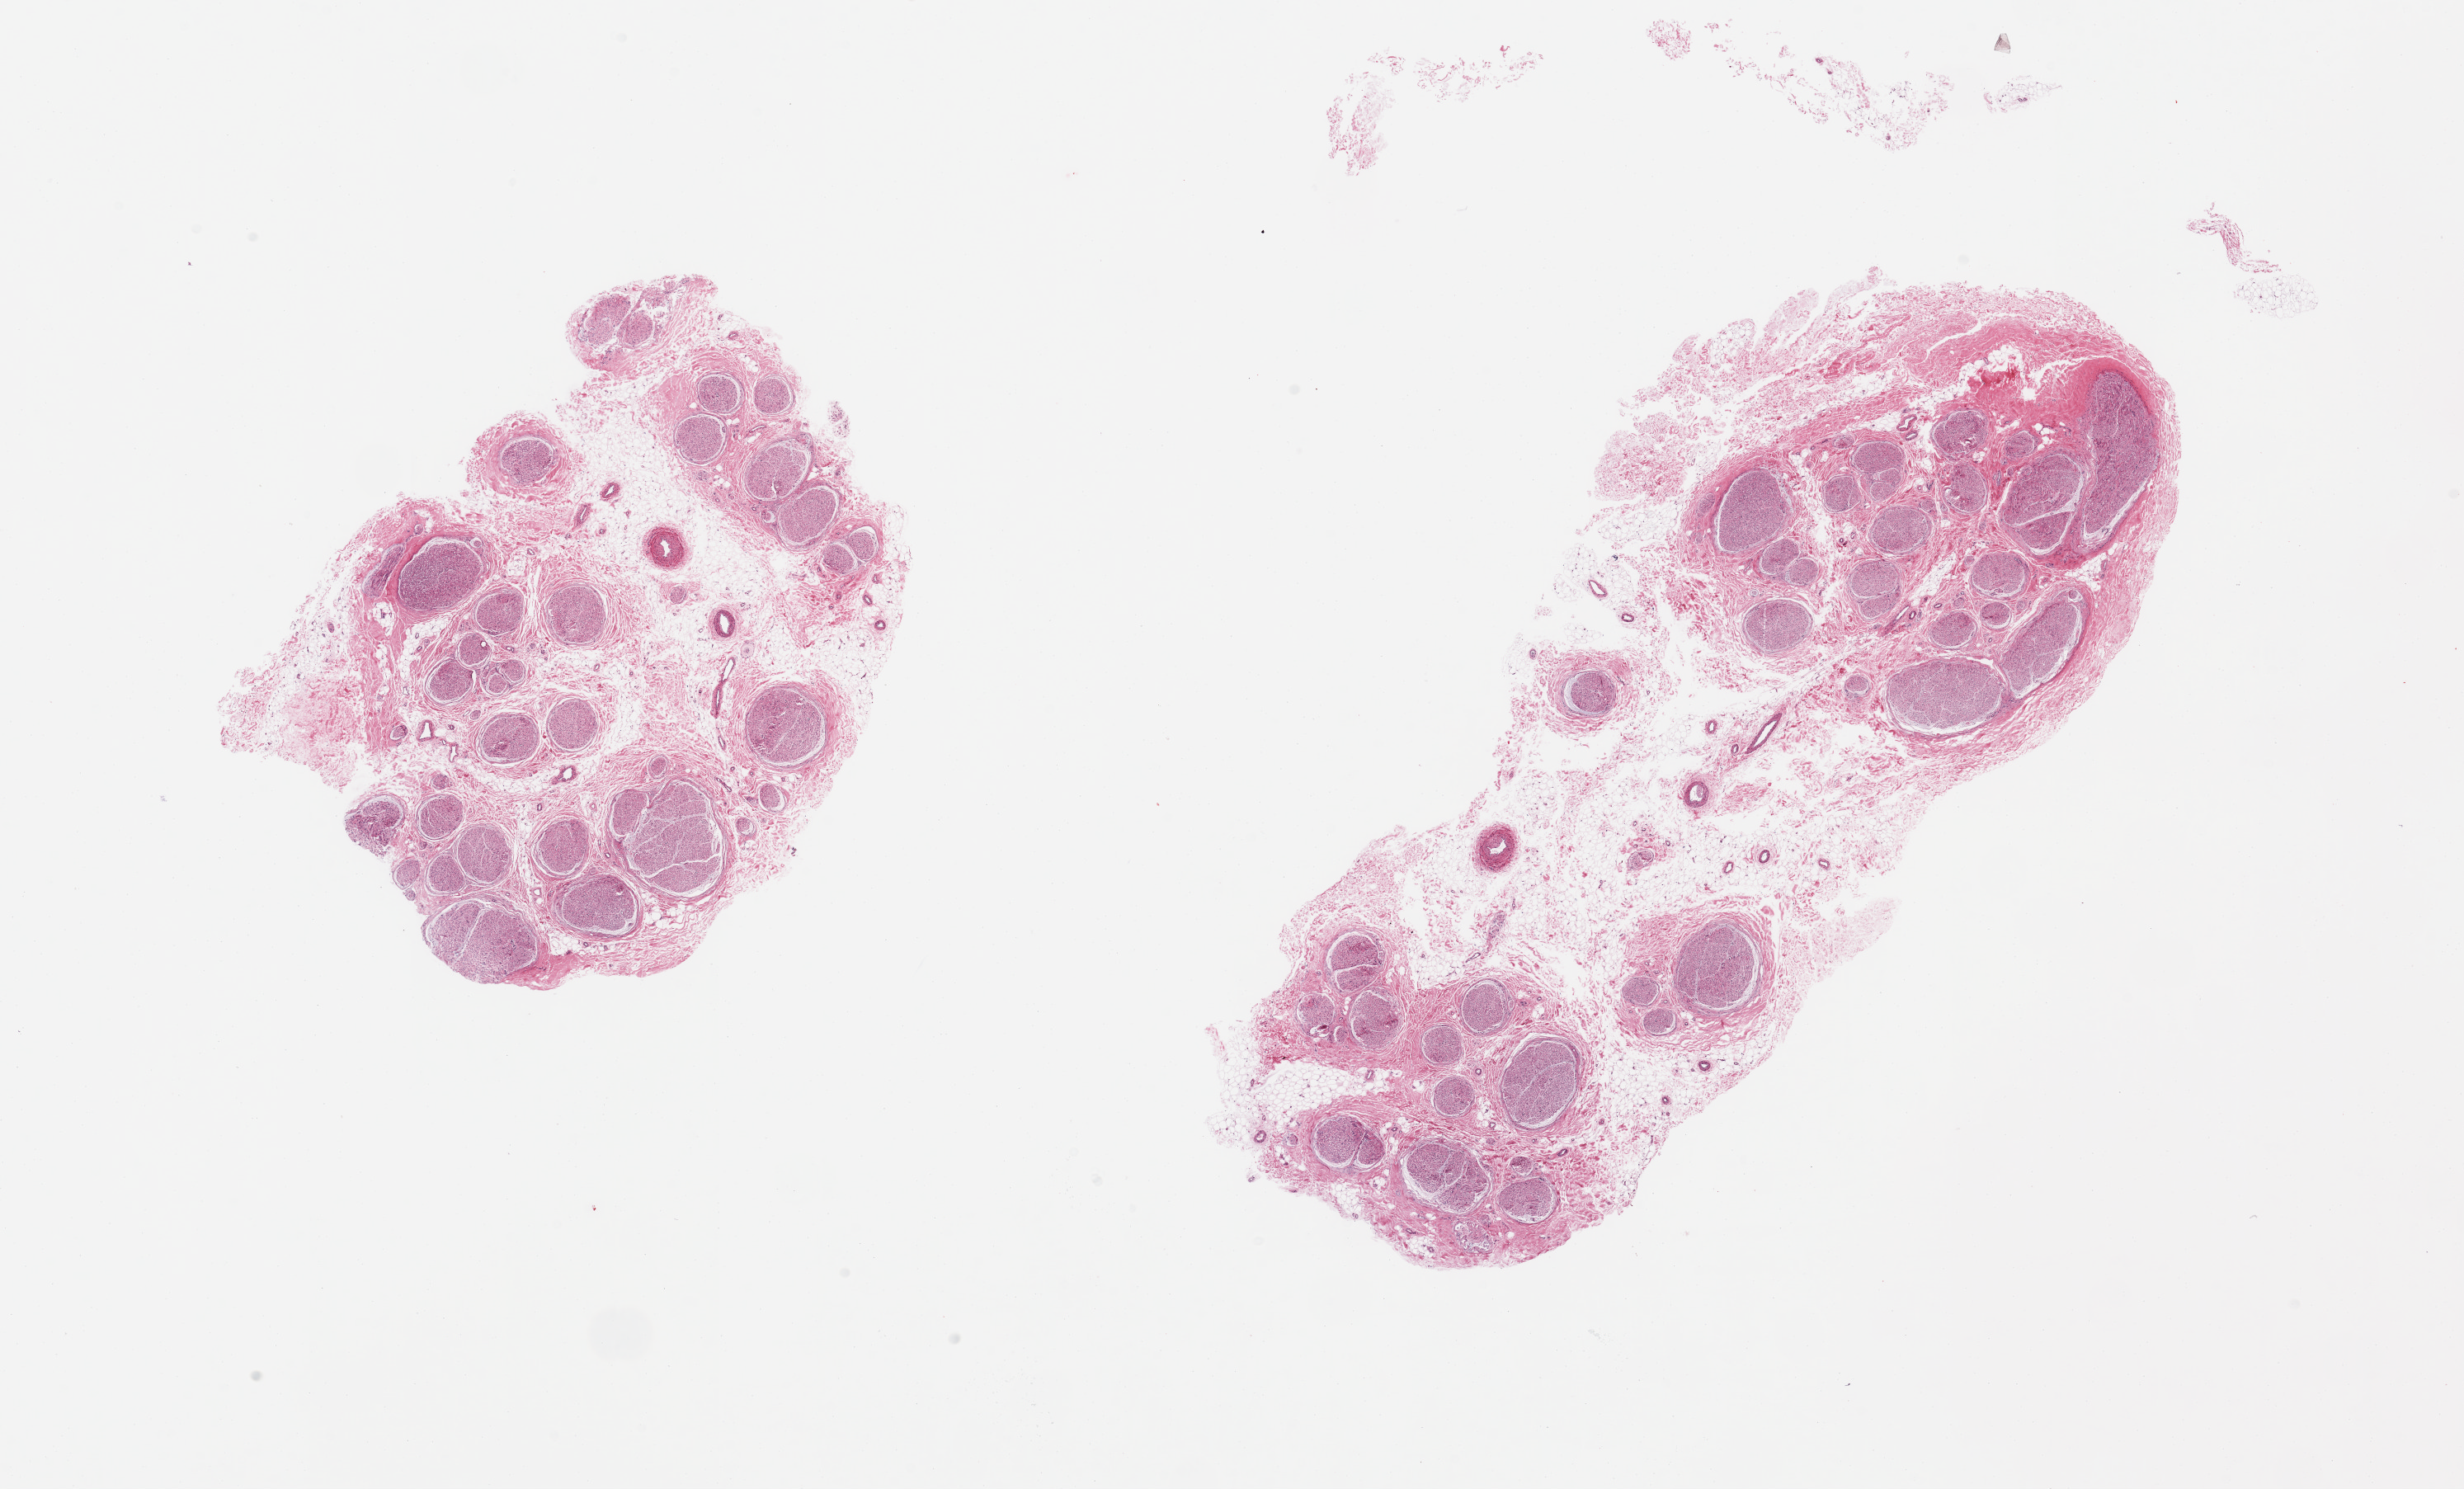
Hematoxylin and eosin (H&E) whole-slide image — a low-resolution overview of the entire scanned area, about 23.6 x 14.3 mm; PAXgene-fixed, paraffin-embedded tissue; target tissue: tibial nerve; tissue donor sample. Donor sex: male.
Reviewer comment on this tissue sample: 2 pieces; 30-60% fat and epineurium.